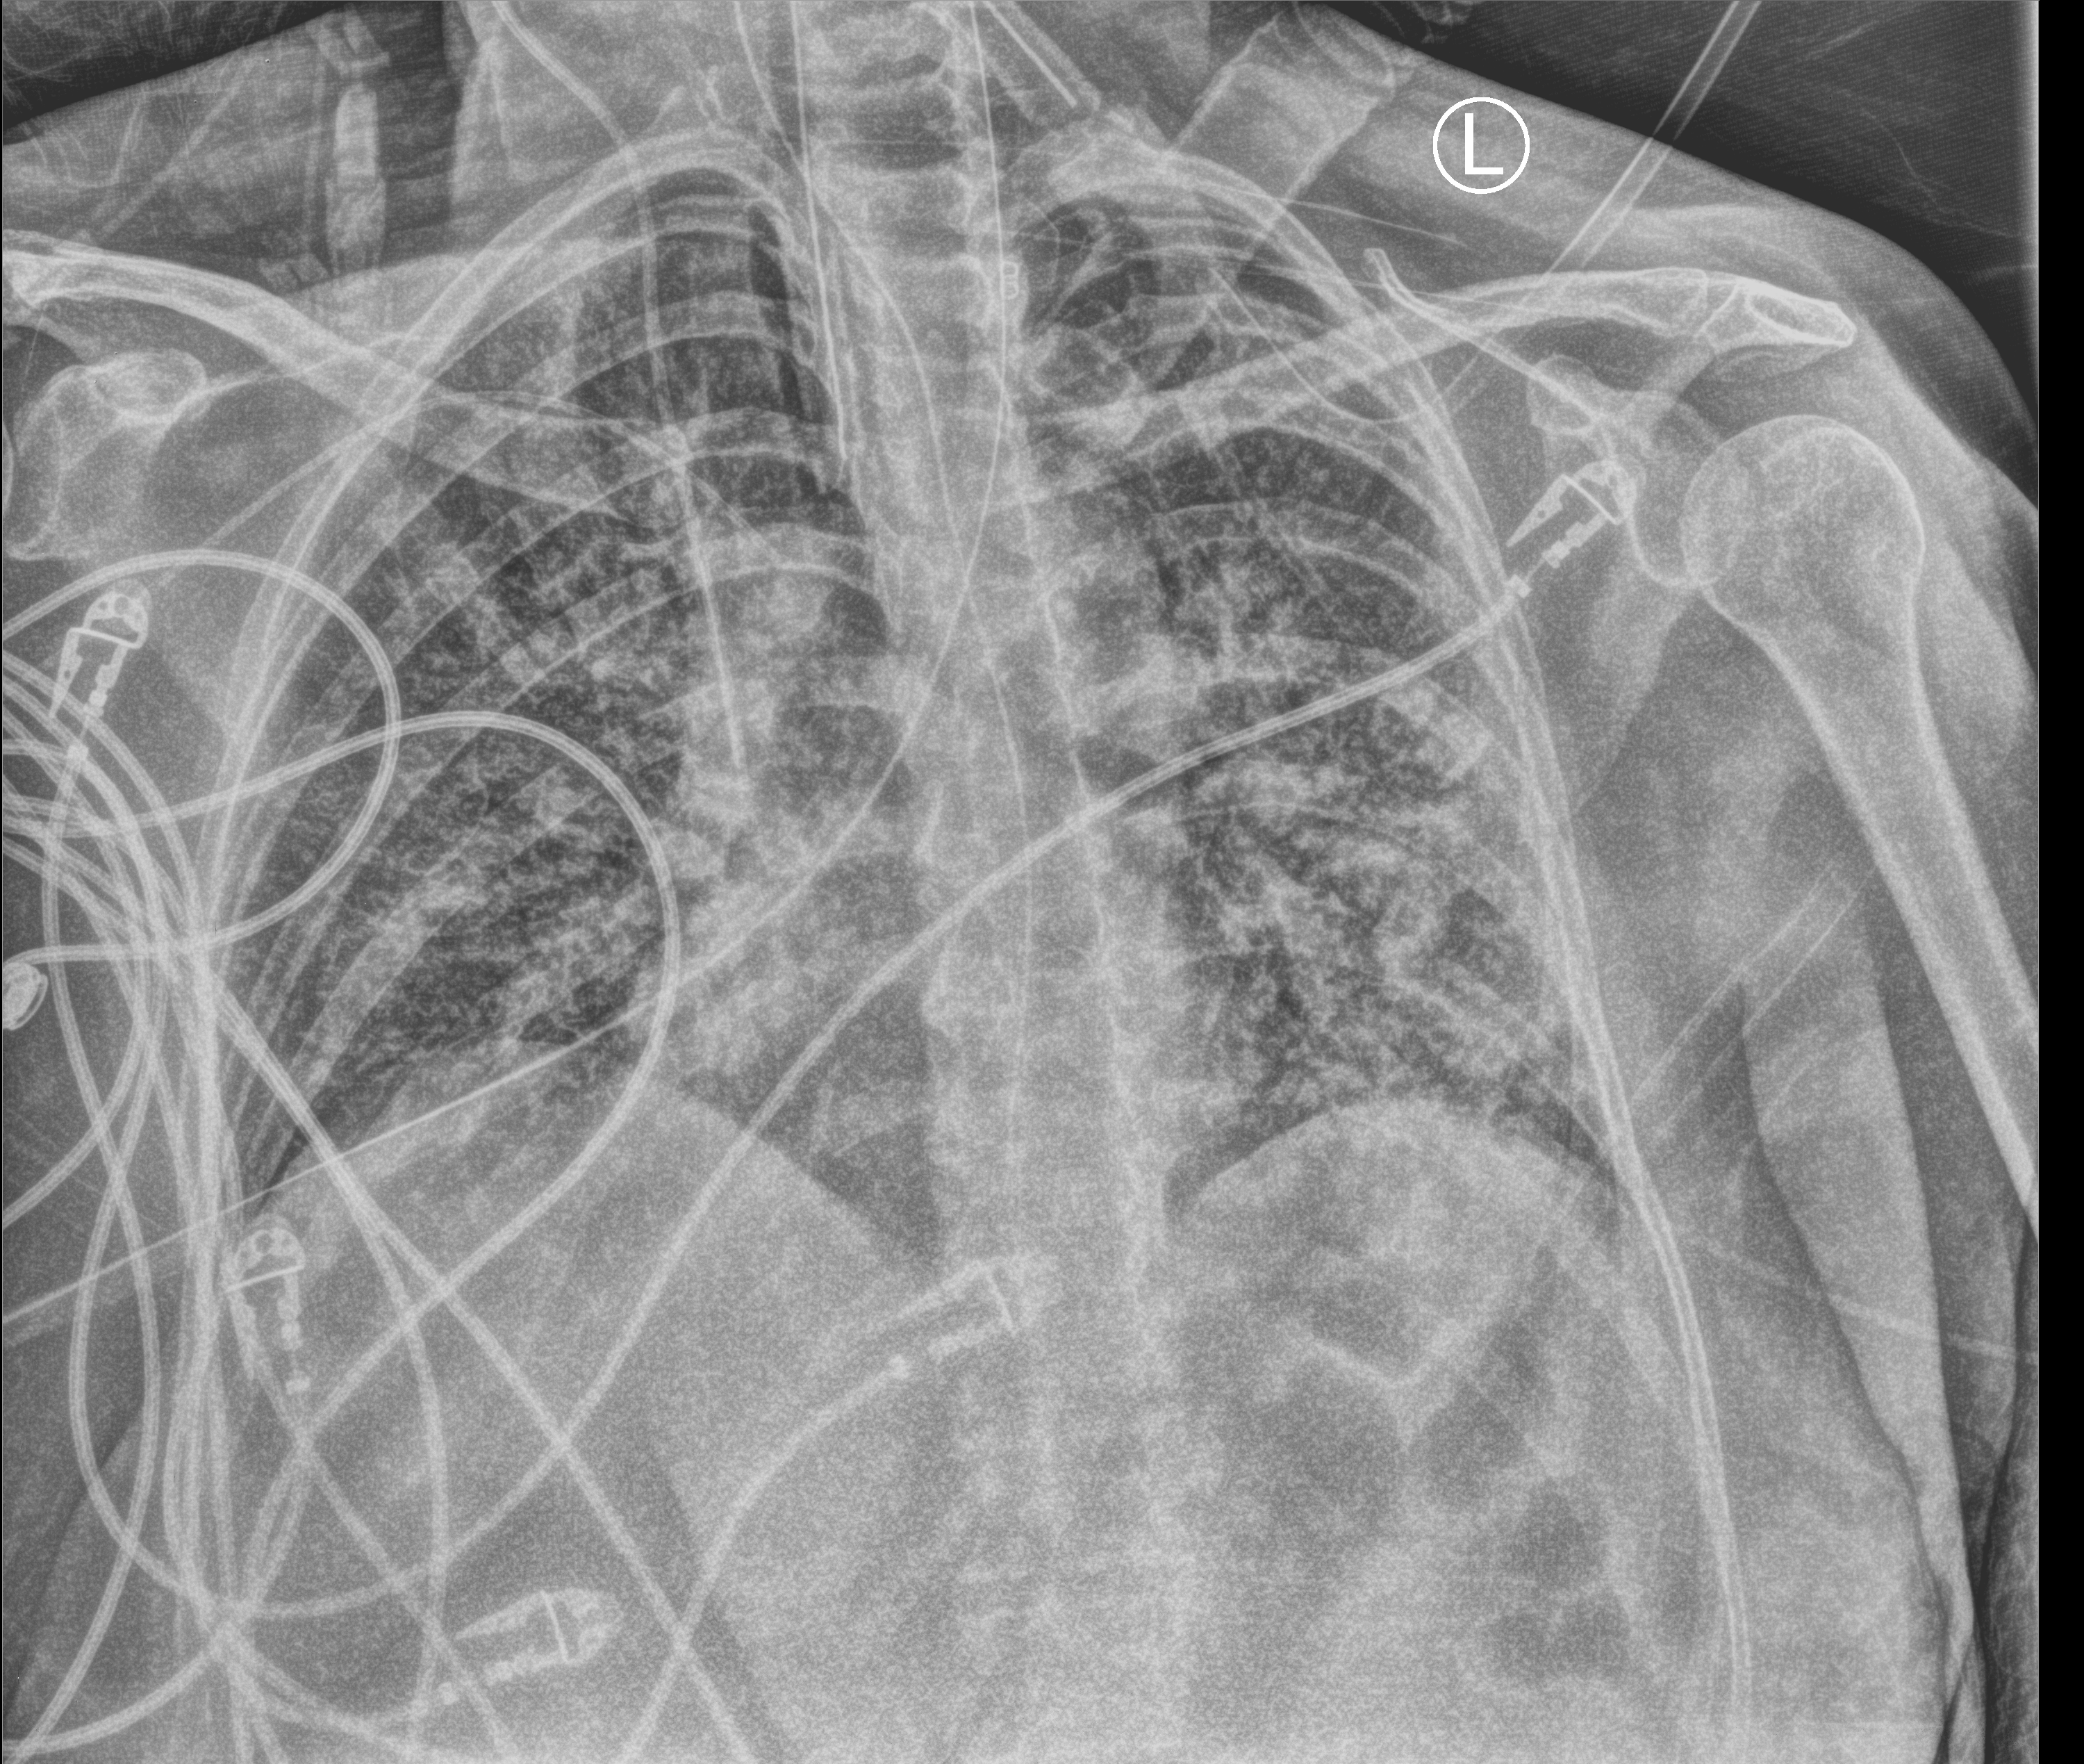
Portable chest radiograph; anteroposterior (AP) projection. Female patient hospitalised with COVID-19, age 60–74 years.
Admission-level facts for this patient (not findings on this image; timing relative to this image not recorded): mechanically ventilated during this hospital stay: yes; admitted to intensive care during this hospital stay: yes.